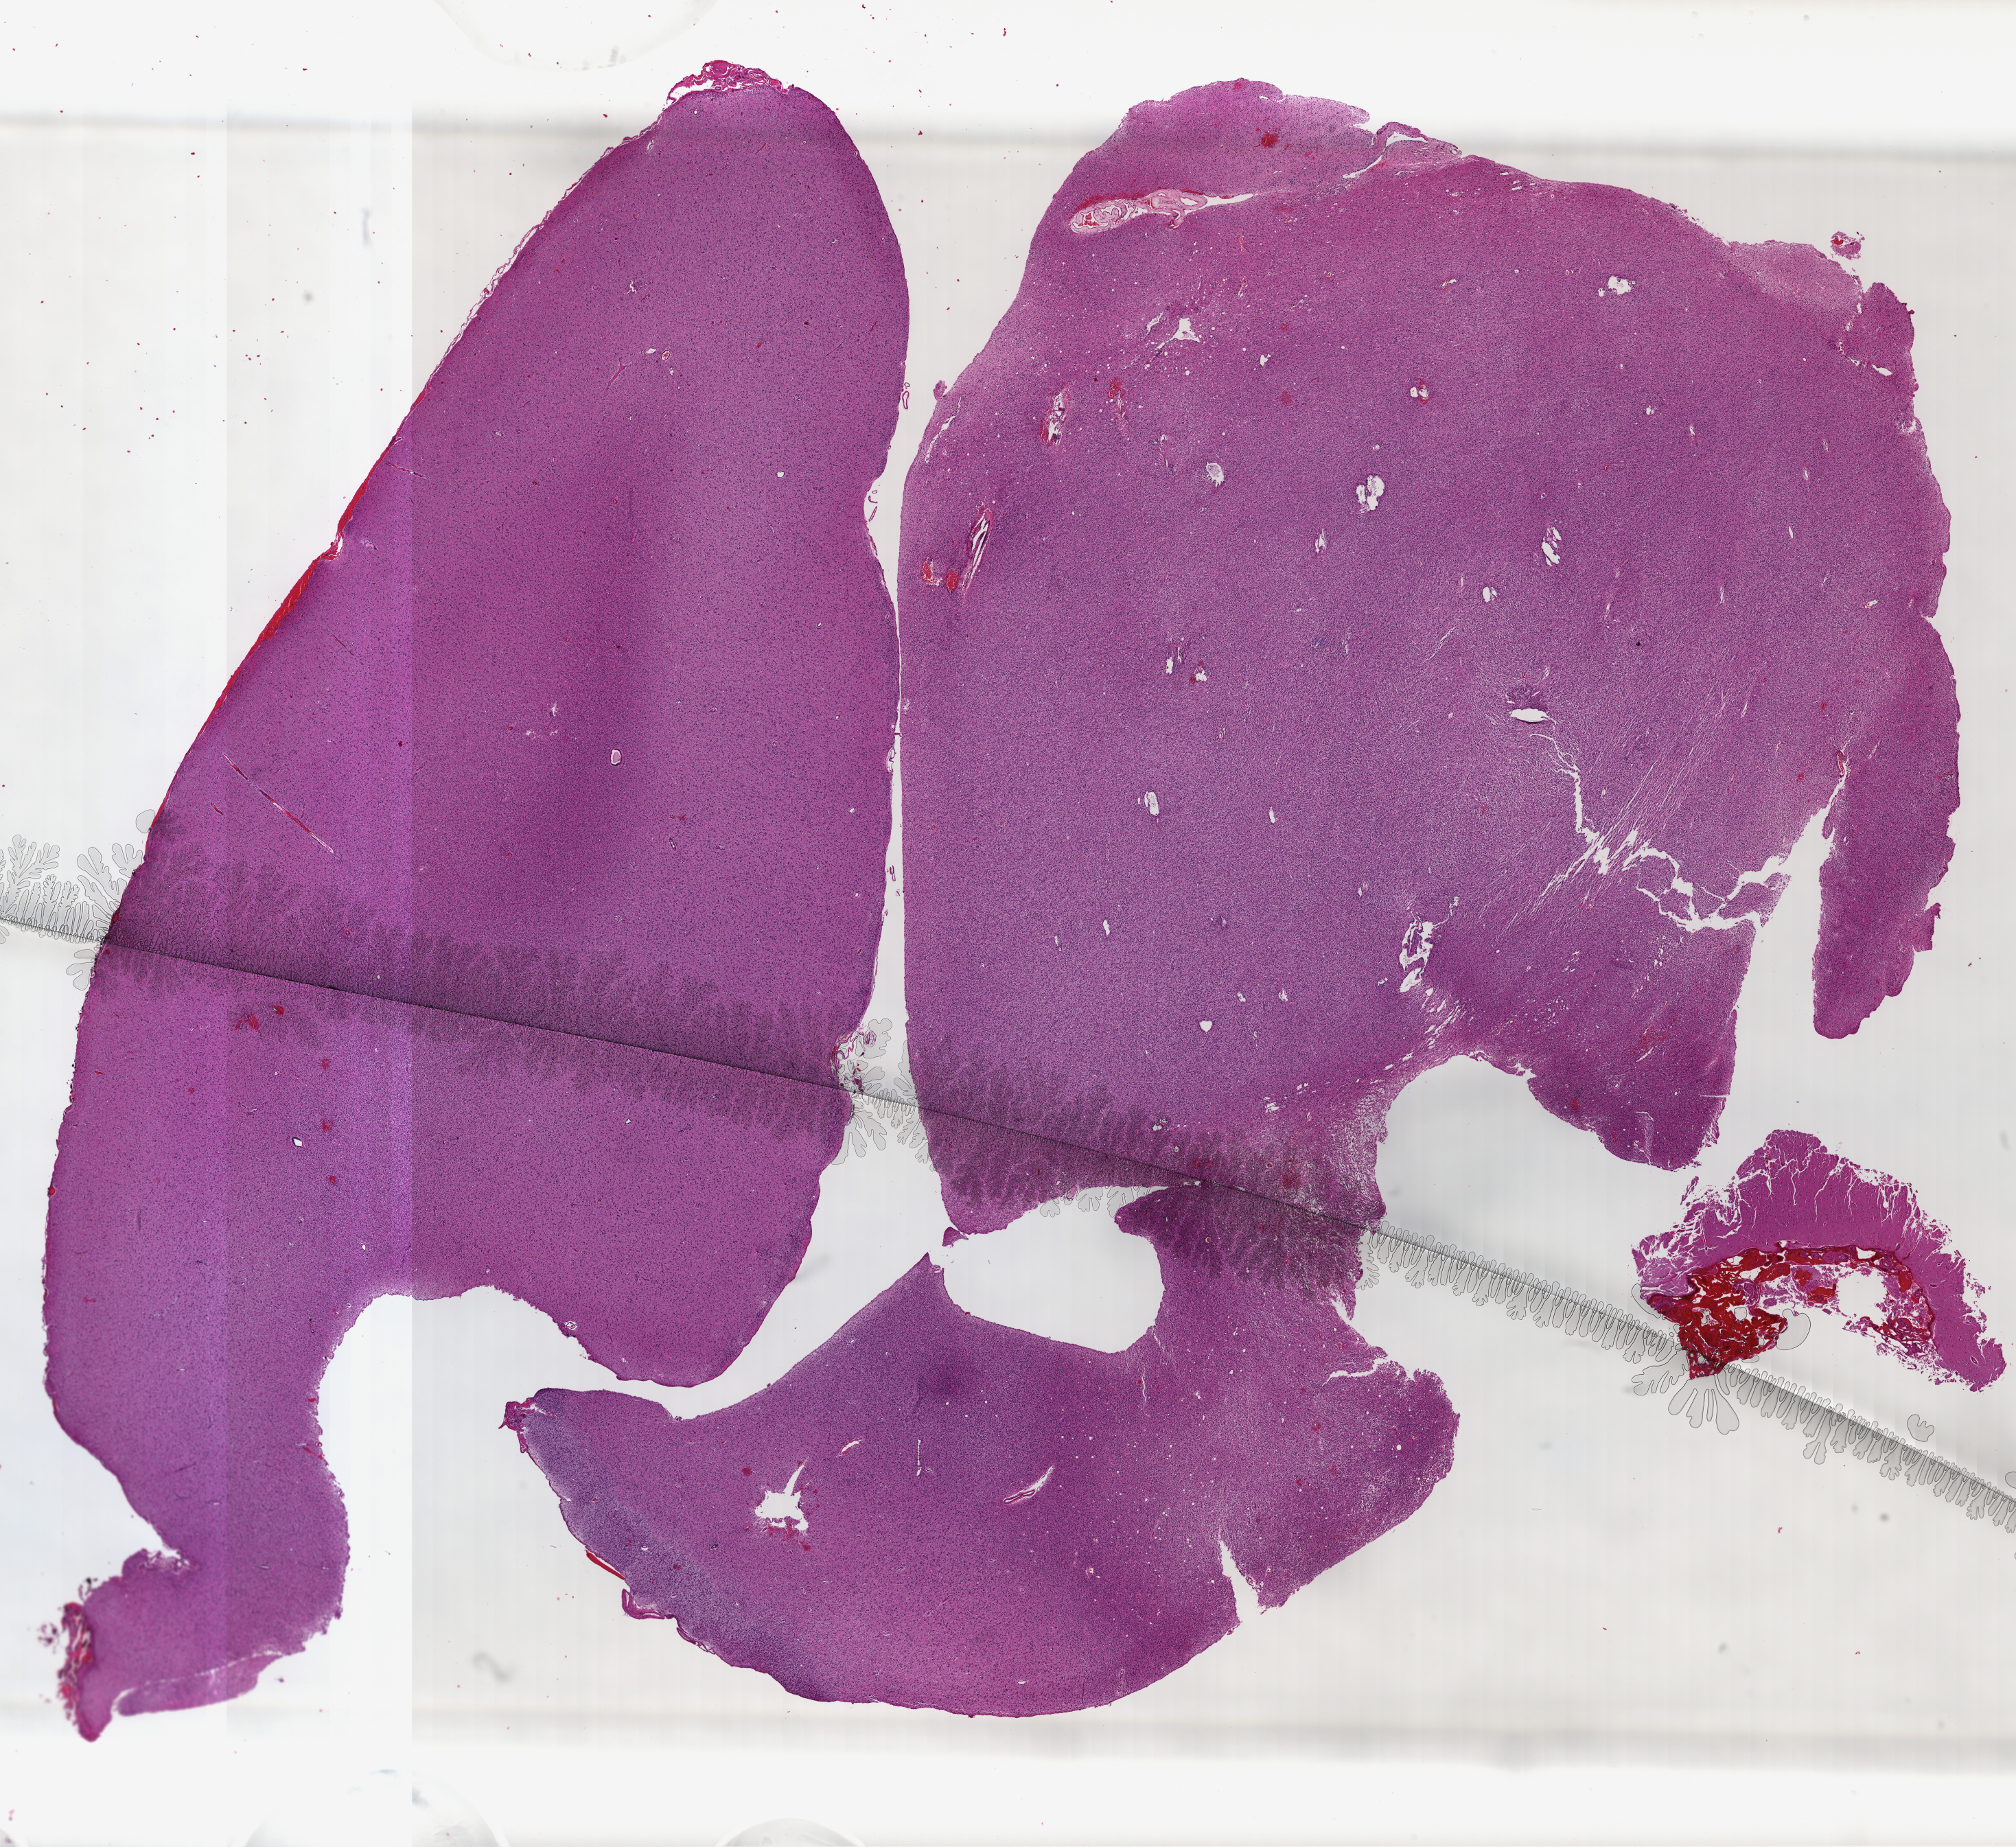
Whole-slide histology image, Hematoxylin and eosin (H&E) stained — a low-resolution overview of the entire scanned area, about 23.7 x 21.7 mm; formalin-fixed paraffin-embedded (FFPE) diagnostic section; brain, primary tumour sample. Female, age 42 years at initial diagnosis. Histologic grade: G3 (poorly differentiated).
Laterality: right. Pathologic diagnosis: Mixed glioma (cerebrum).